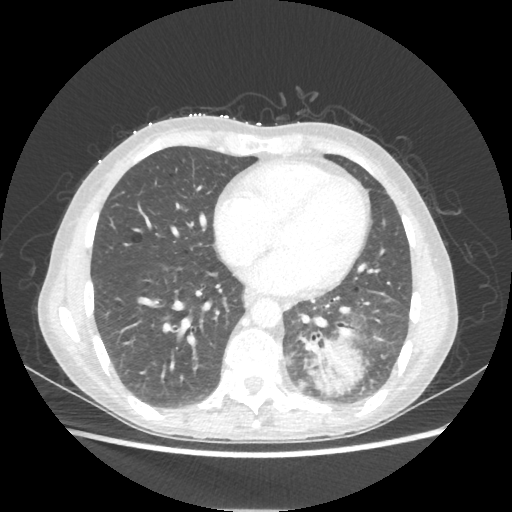
Chest CT, one axial slice; slice 86 of 221 in the series (ordered by position); 80 kVp; lung window (W 1500 / L -600 HU); 512 × 512 image matrix. Patient: female, 53 years. From the clinical record (not read from this slice): clinical TNM (as recorded): T3 N0 M0.
Structures marked on this image (rectangle marked by the reading radiologist):
- lung tumour (recorded histology: adenocarcinoma): bounding box <304,336,362,394> (left, top, right, bottom; pixels)